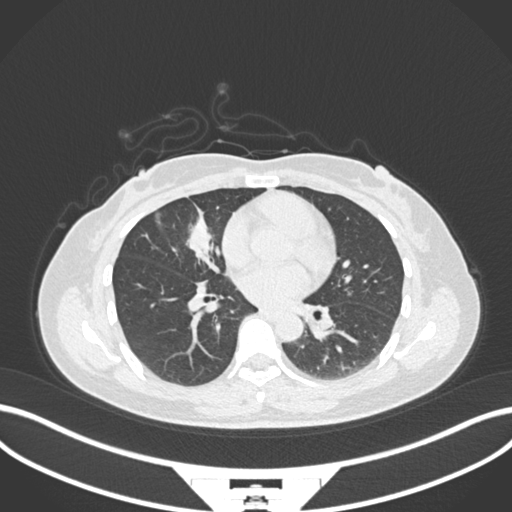
Chest CT, one axial slice. Position 79 of 171 along the scan axis. 120 kVp. Lung window (W 1500 / L -600 HU). 512 × 512 image matrix, field of view 400 × 400 mm. Female patient, age 43 years. From the clinical record (not read from this slice): clinical TNM (as recorded): T1c N3 M1.
Outlined on this slice (bounding box drawn by a radiologist):
- lung tumour (recorded histology: adenocarcinoma): box from (x=185, y=207) to (x=217, y=268) px